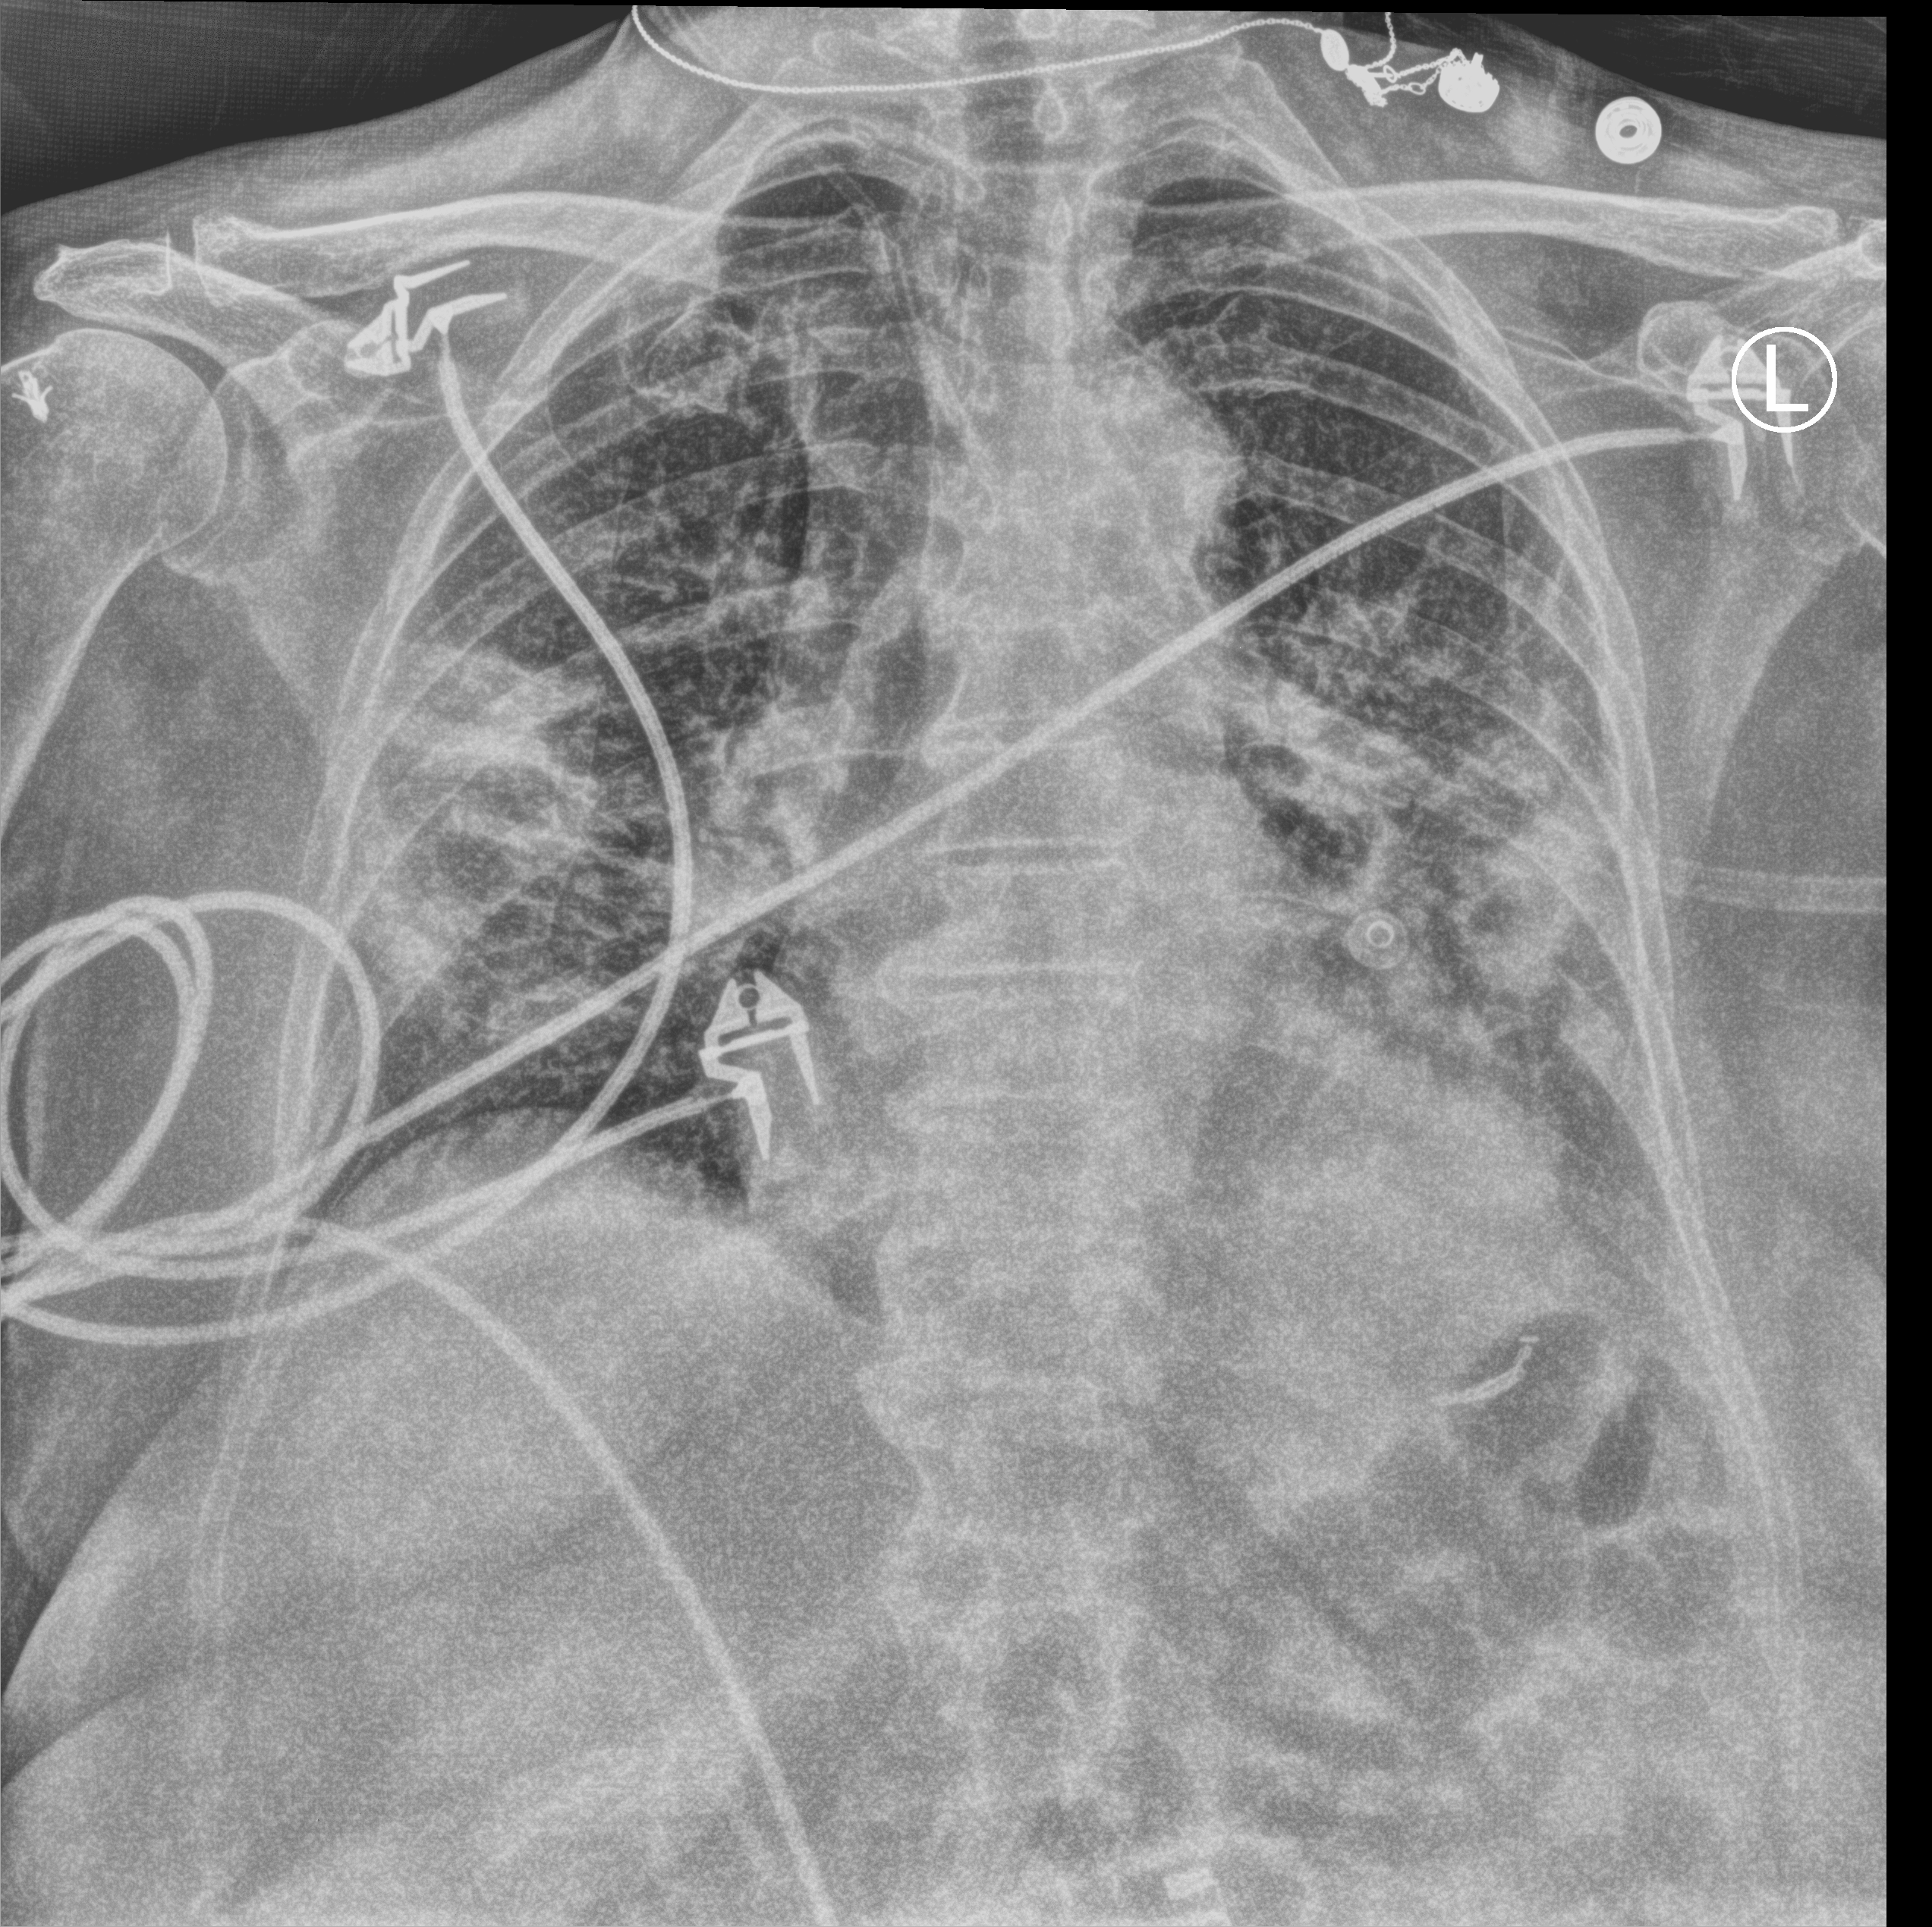
Portable chest radiograph; anteroposterior (AP) projection. Patient hospitalised with COVID-19; female, aged 60–74 years.
Admission-level facts for this patient (not findings on this image; timing relative to this image not recorded): admitted to intensive care during this hospital stay: no.